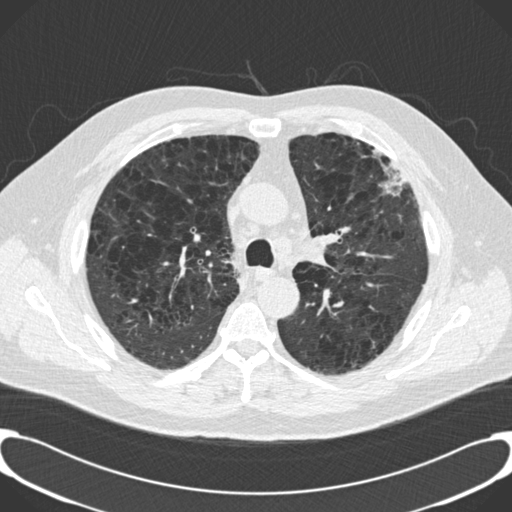
Chest CT (low-dose screening protocol), one axial image, third annual screen, lung window (W 1500 / L -600 HU), 2 mm slice thickness, slice 52 of 189 in the series, 512 × 512 image matrix. Male participant, aged 59 years at enrolment.
Expert-annotated lung lesion, bounding box <357,145,421,220> (left, top, right, bottom; pixels). Screening reader's record for this exam: no non-calcified nodule ≥4 mm recorded. Lung cancer was diagnosed 134 days after this screen: bronchiolo-alveolar carcinoma, mixed mucinous and non-mucinous, left upper lobe, stage IA (AJCC 6th edition), 20 mm at pathology.